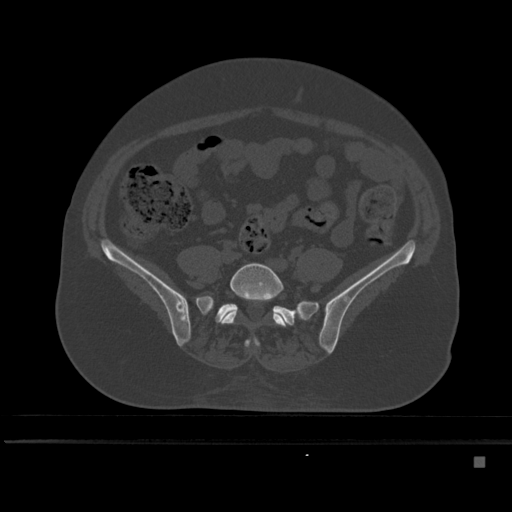
CT including the spine, one axial slice; position 103 of 495 along the scan axis; bone window (W 1800 / L 400 HU); 1.5 mm slice thickness; 512 × 512 image matrix, field of view 404 × 404 mm. Patient: female, 33 years. Case-level facts recorded for this patient, not image findings: primary cancer: breast; vertebrae with lytic lesions (as recorded): T1.
Outlined on this slice (semi-automatically segmented with operator editing):
- L5 vertebra: bounding box [x1, y1, x2, y2] px = [221, 263, 288, 348]